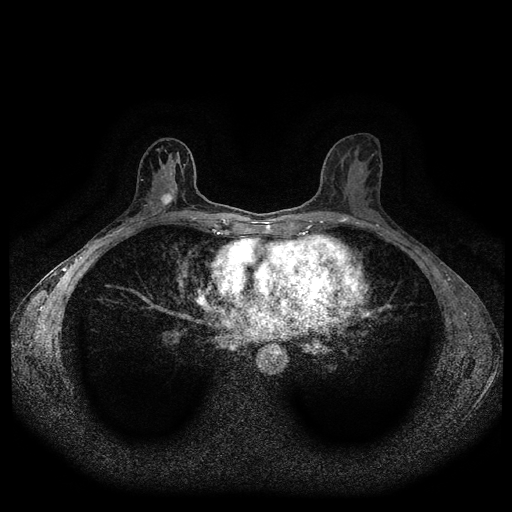
Breast MRI (dynamic contrast-enhanced, multi-phase), one axial slice; position 55 of 116 along the scan axis; dynamic contrast-enhanced series, time point 2 of 5 at this slice position (early post-contrast); 1.5 T; TE 2.6 ms, TR 5.3 ms; 2 mm slice thickness; 512 × 512 image matrix. Patient: female, 50 years.
Annotated regions visible in this slice (semi-automatically segmented with operator editing):
- breast lesion (labelled 'tumour' in the annotation; benign lesions carry a separate 'benign' label): bounding box <157,192,175,208> (left, top, right, bottom; pixels)